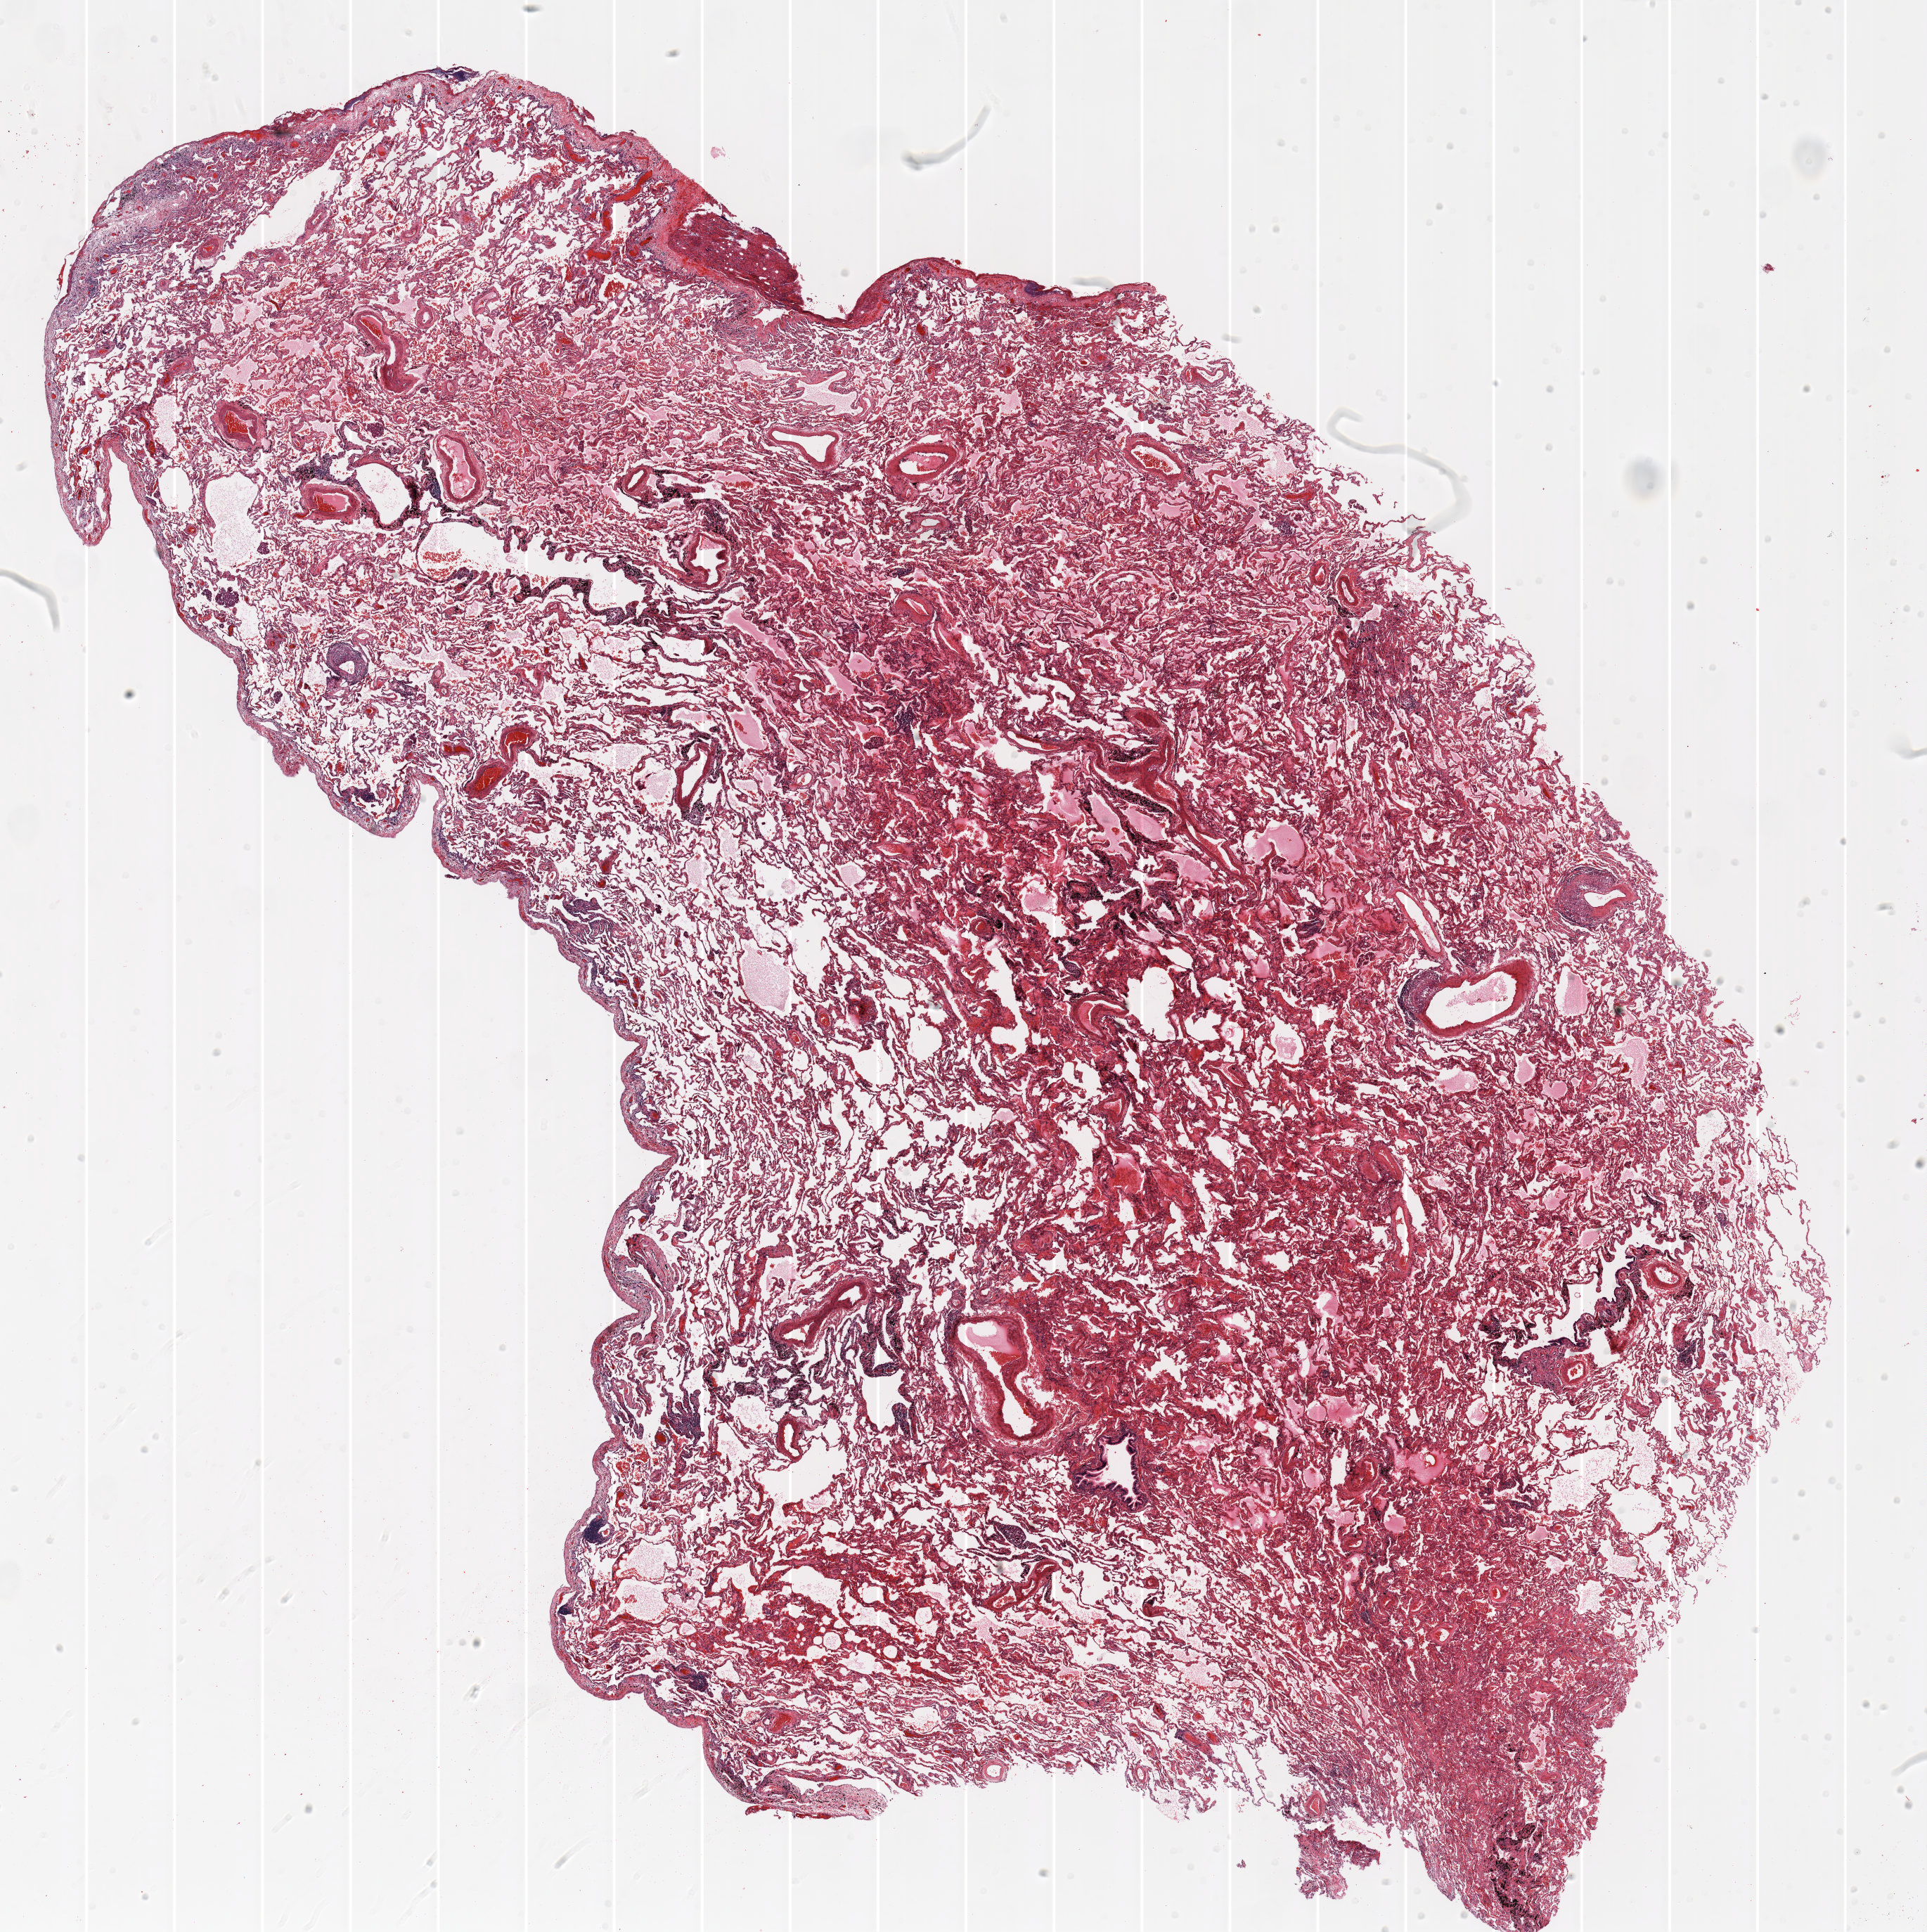
Hematoxylin and eosin (H&E) stained whole-slide image, shown as a low-resolution overview of the whole scanned area (about 22.0 x 22.1 mm). FFPE section. Lung. Female, age 72 at enrolment. Former smoker at enrolment. Grade: well differentiated (G1).
ICD-O-3 topography: upper lobe of lung (C34.1). Stage (AJCC 6th edition): IA. Primary tumour location (clinical record): right upper lobe. Tumour size (pathology): 8 mm. Participant's lung-cancer diagnosis: Bronchiolo-alveolar adenocarcinoma, NOS (ICD-O-3 8250/3).